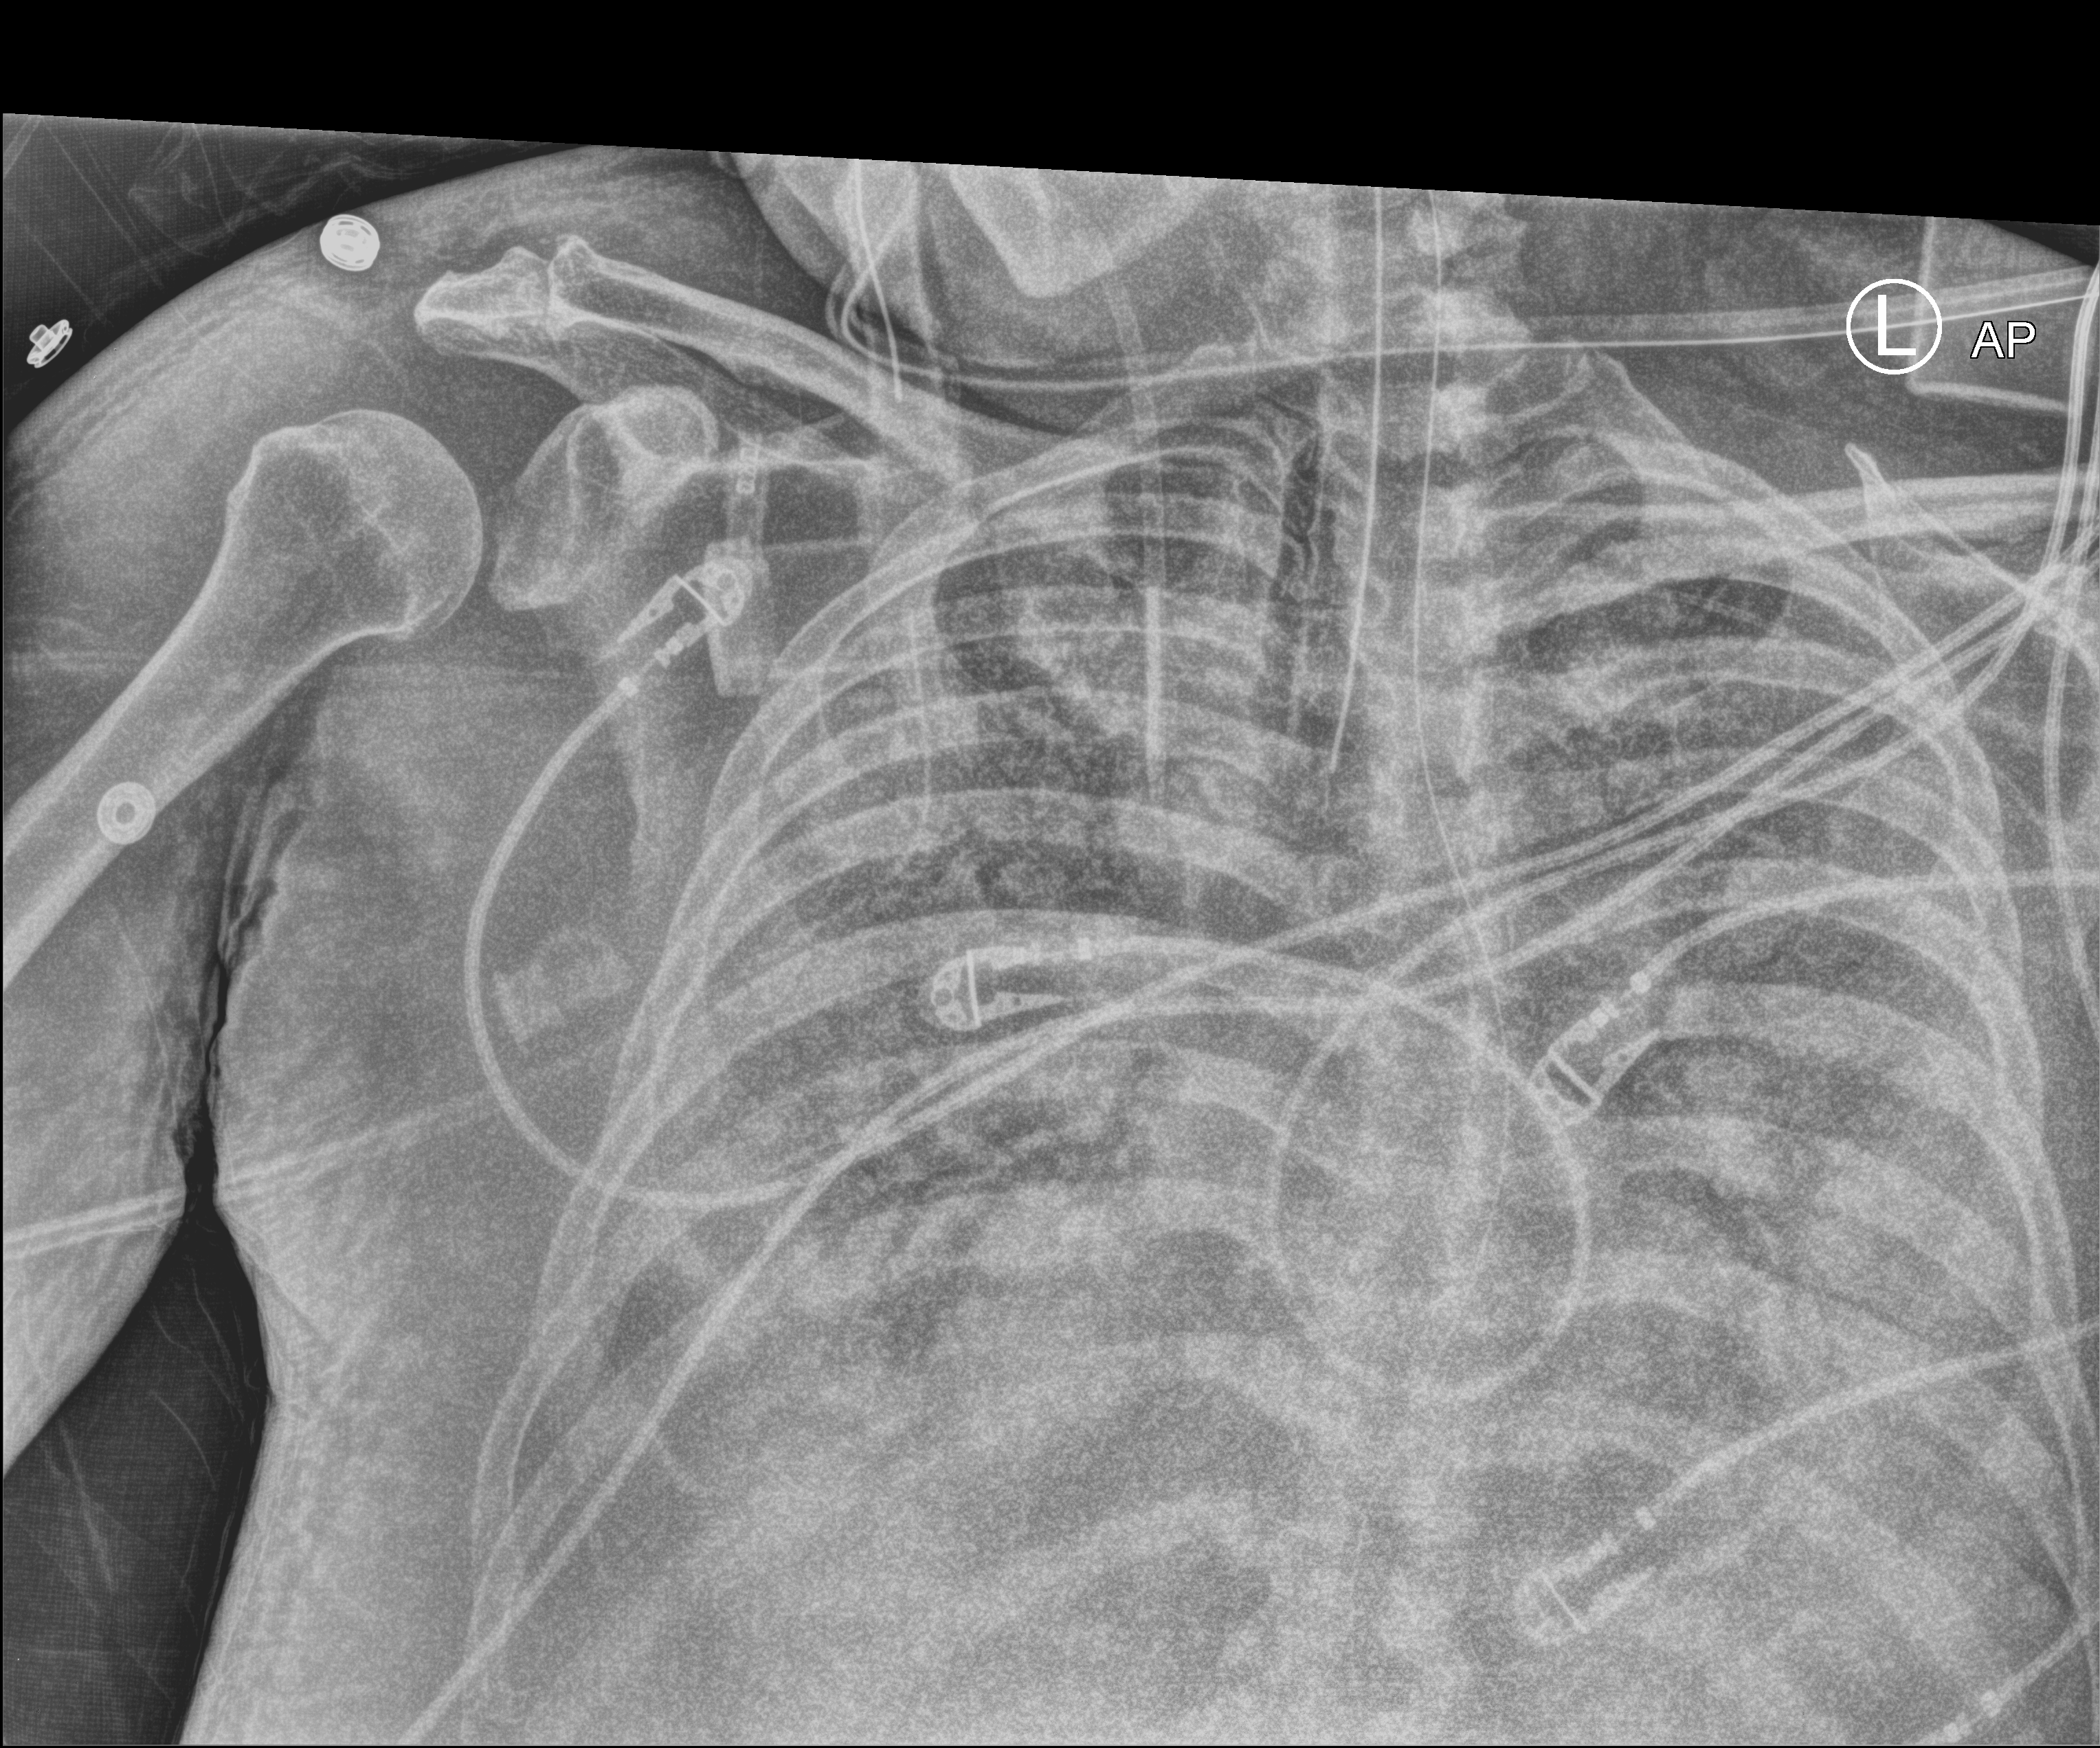
Portable chest radiograph, anteroposterior (AP) projection. Male patient hospitalised with COVID-19, age 60–74 years.
Admission-level facts for this patient (not findings on this image; timing relative to this image not recorded): smoking status (admission record): never; length of hospital stay: 28 days; mechanically ventilated during this hospital stay: yes.